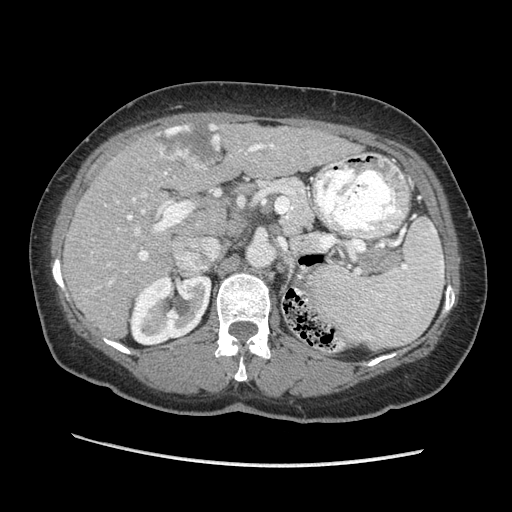
Contrast-enhanced abdominal CT (liver protocol), one axial slice. Position 127 of 170 along the scan axis. Reconstruction kernel STANDARD. Soft-tissue window (W 400 / L 40 HU). 2.5 mm slice thickness. 512 × 512 image matrix, field of view 360 × 360 mm. Case-level facts recorded for this patient, not image findings: diagnosis: hepatocellular carcinoma (patient treated with transarterial chemoembolisation; whether this scan precedes or follows treatment is not stated here); TNM stage (as recorded): Stage-II; Child-Pugh class: A; tumour size: 4 cm.
Annotated regions visible in this slice (semi-automatic segmentation, software-assisted and operator-edited):
- liver parenchyma outside the tumour (the mass and vessels are separate outlines, so this box may not span the whole liver): box from (x=64, y=122) to (x=360, y=336) px
- mass: (x=157, y=123)–(x=221, y=170)
- liver vessels: (x=105, y=143)–(x=274, y=285)